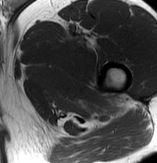
MRI of an extremity soft-tissue mass, one axial slice. MR volume resampled by the dataset authors to the PET/CT grid (not the native acquisition matrix). 157 × 163 image matrix, field of view 153 × 159 mm. Male patient. Case-level facts recorded for this patient, not image findings: histological type: extraskeletal osteosarcoma; grade: high; site of the primary tumour: left adductur.
Outlined on this slice (expert contour drawn on MRI and transferred to this co-registered scan by the dataset authors):
- gross tumour volume (mass): bounding box <26,23,128,121> (left, top, right, bottom; pixels)